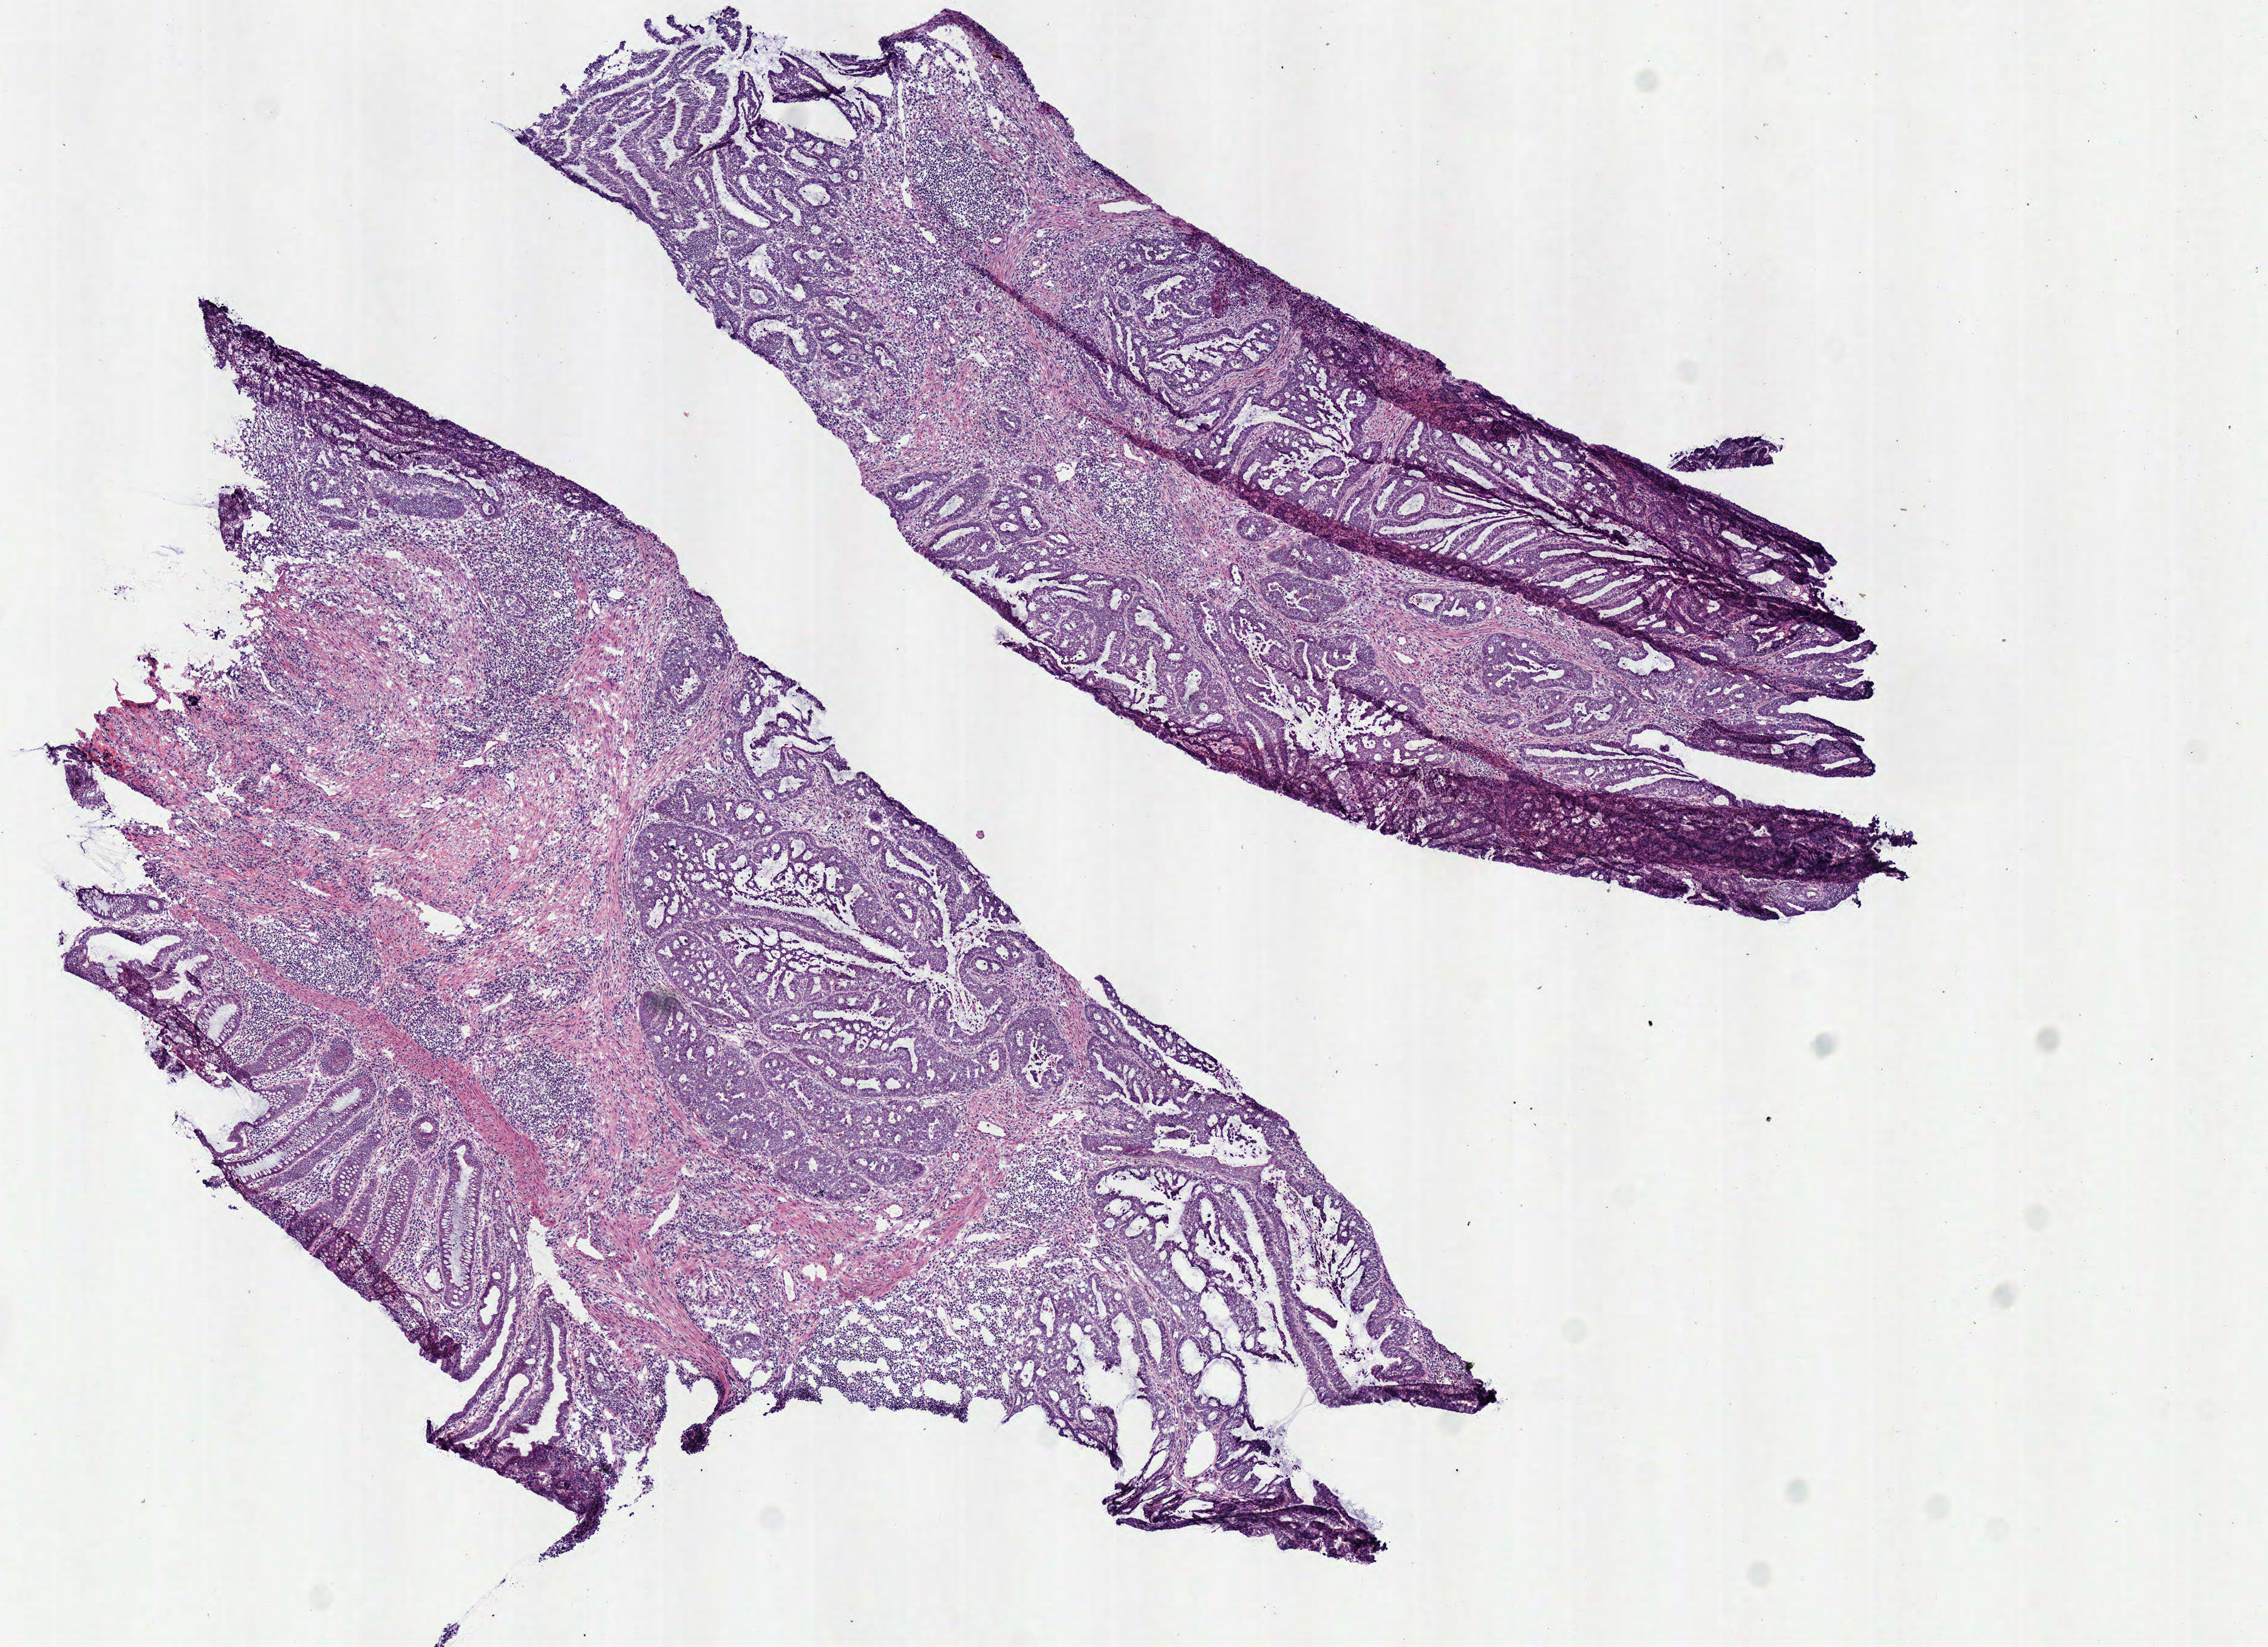
Hematoxylin and eosin (H&E) stained whole-slide image — low-resolution overview of the scanned area, about 7.3 x 5.3 mm. Frozen section from the bottom of the tissue portion. Primary tumour sample from the colon. Female, age 60 years at initial diagnosis. Slide review estimates, as recorded: tumour cells 68%, tumour nuclei 65%.
Diagnosis: Adenocarcinoma, NOS (cecum).